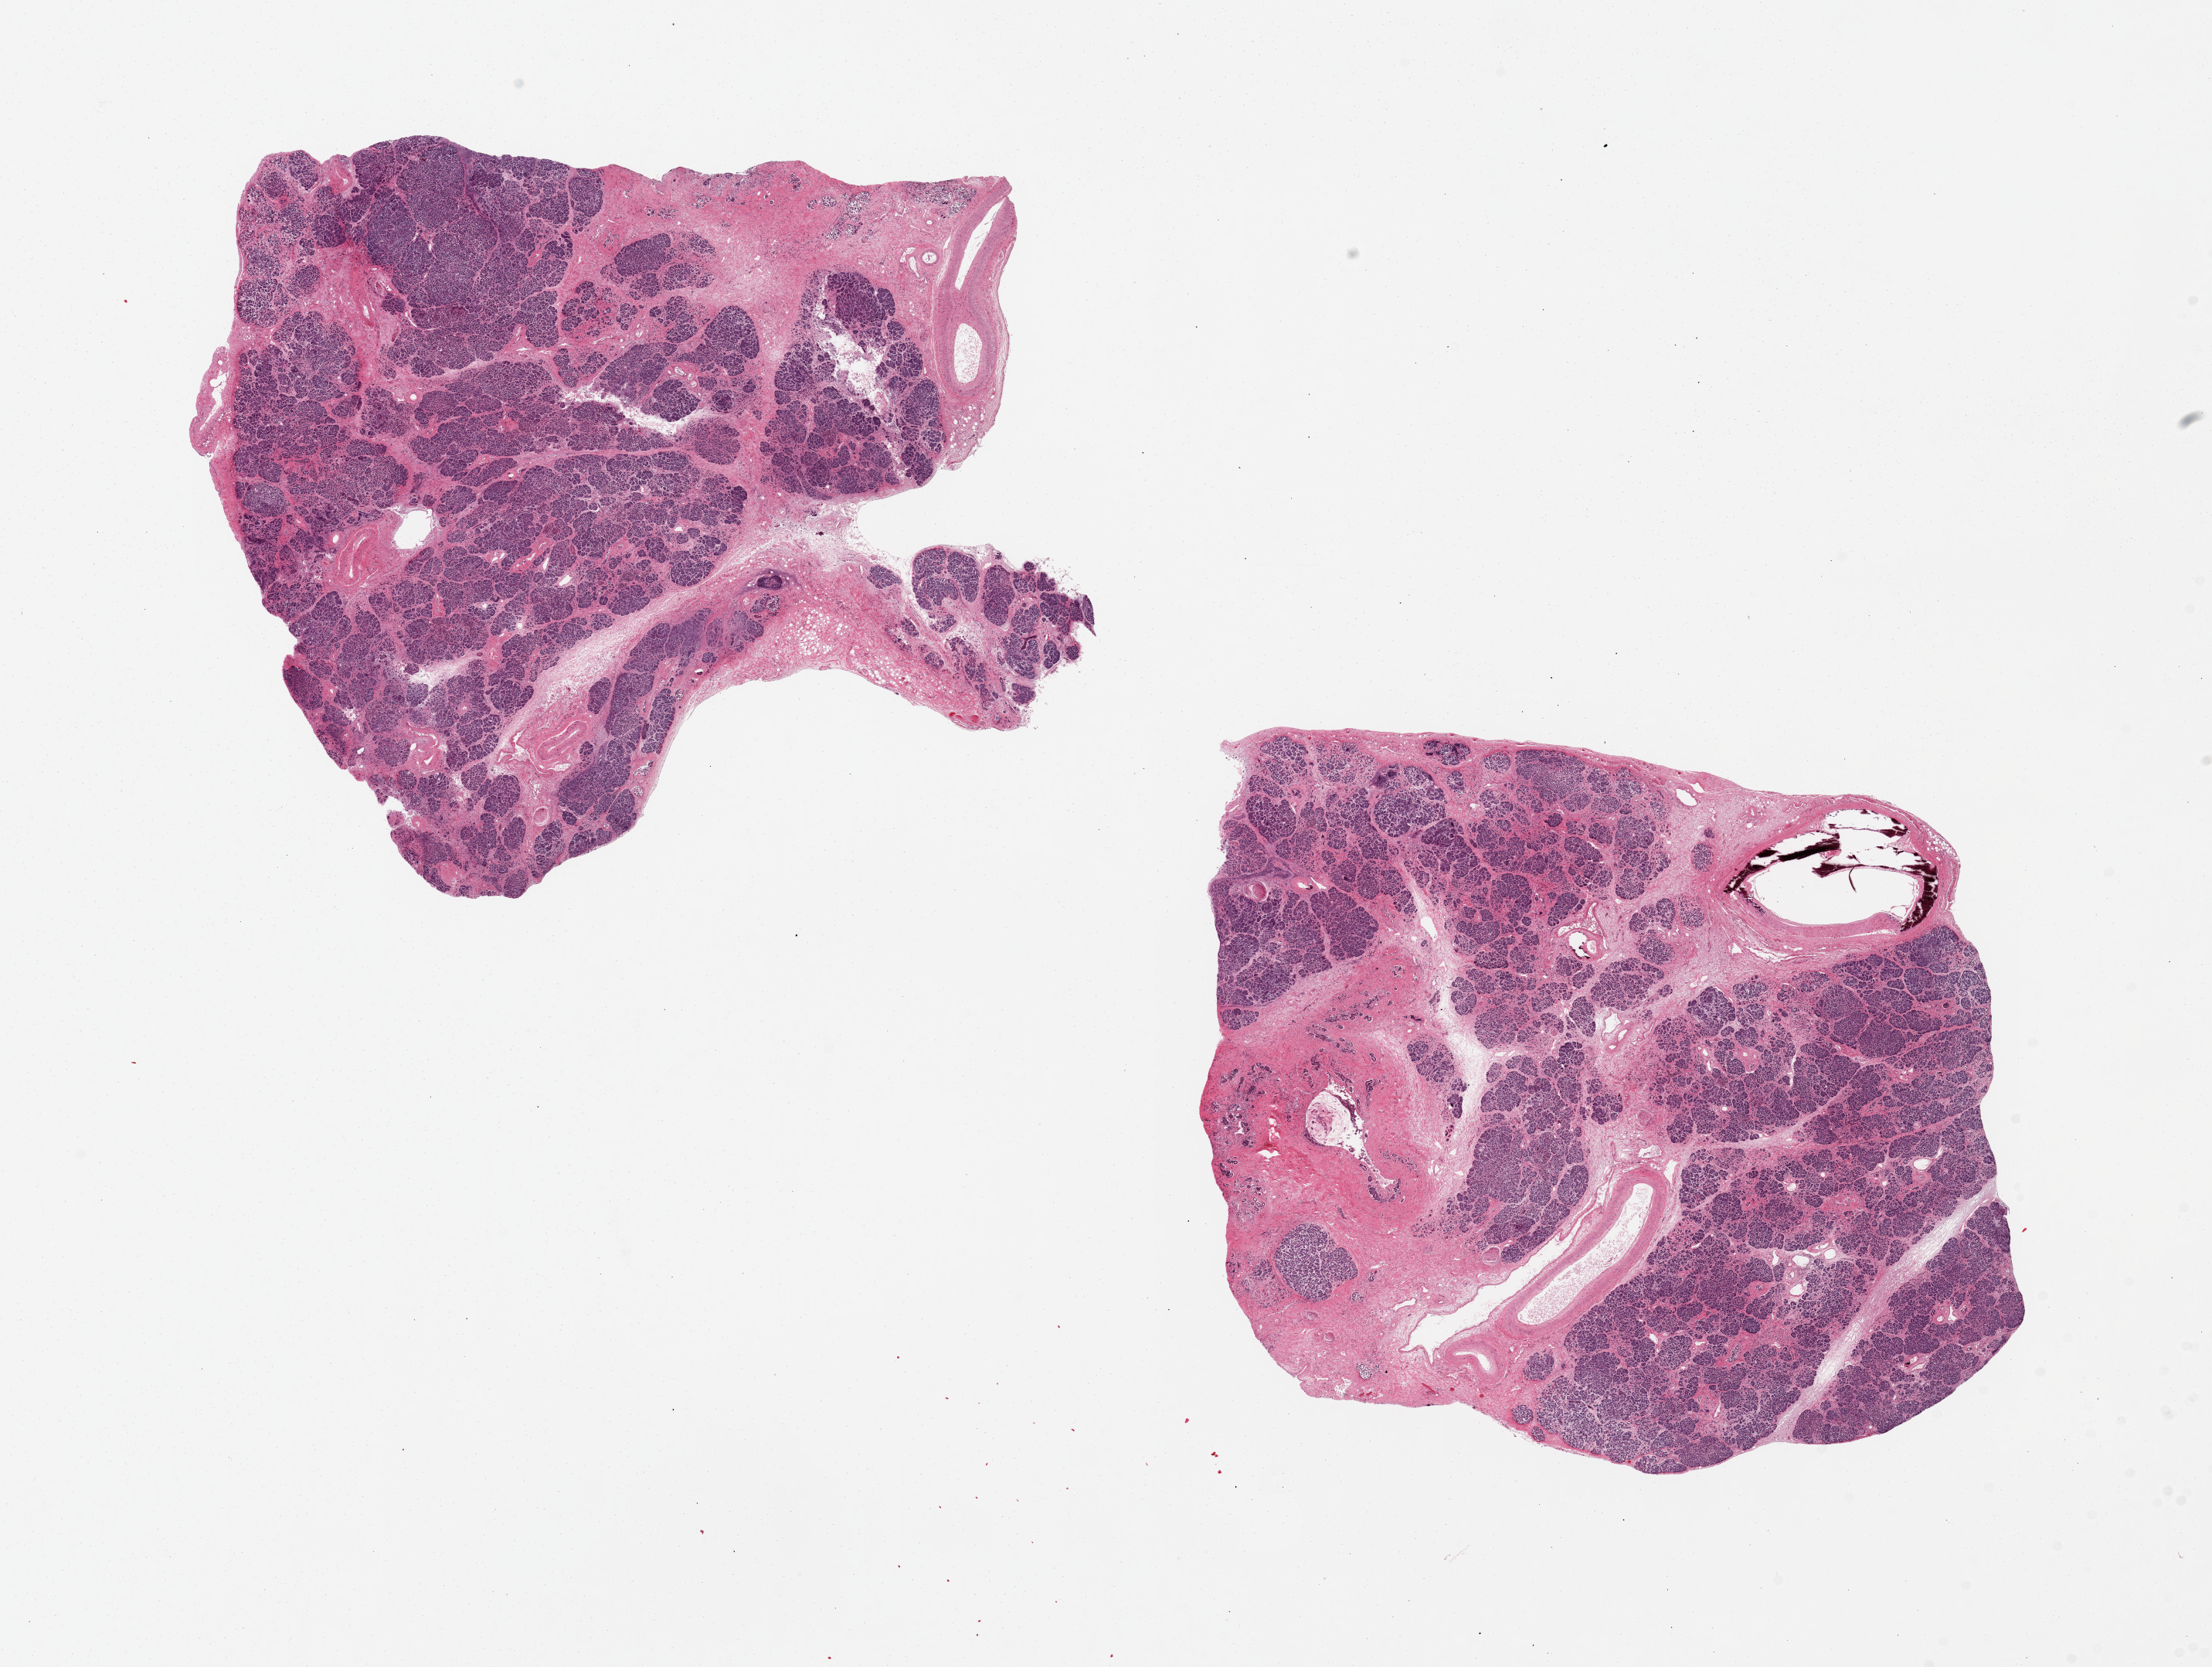
Whole-slide image, hematoxylin and eosin (H&E) stain — shown as a low-resolution overview of the whole scanned area (about 22.6 x 17.1 mm, acquisition: 20x scan), PAXgene-fixed, paraffin-embedded tissue, sampled site (target tissue): pancreas, donor tissue sample.
• pathologist's review note for this sample: 2 pieces; fibrosis with reduction in number of islets